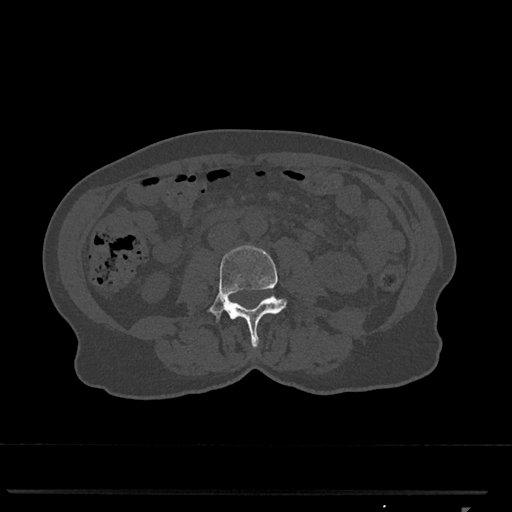
CT including the spine, one axial slice; slice 270 of 793 in the series (ordered by position); 120 kVp; bone window (W 1800 / L 400 HU); 0.5 mm slice thickness; 512 × 512 image matrix, field of view 380 × 380 mm. Patient: female, 62 years. From the clinical record (not read from this slice): primary cancer: renal.
Outlined on this slice (semi-automatic segmentation, software-assisted and operator-edited):
- L3 vertebra: bounding box (x1, y1, x2, y2) in pixels: (209, 245, 287, 349)